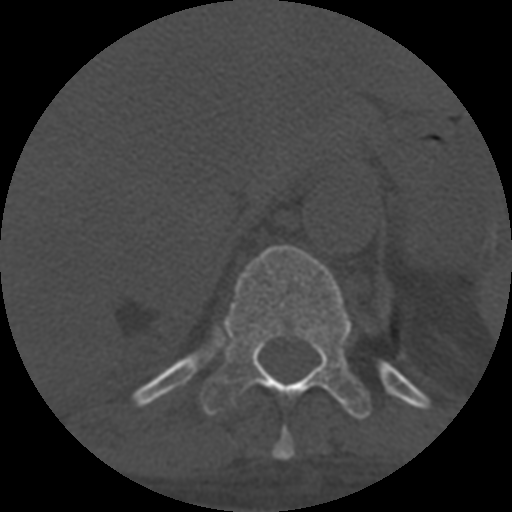
CT including the spine, one axial slice; slice 340 of 708 in the series (ordered by position); reconstruction kernel STANDARD; 120 kVp; one of 3 acquisitions stored at this slice position; bone window (W 1800 / L 400 HU); 512 × 512 image matrix. Patient age 55 years. Case-level facts recorded for this patient, not image findings: primary cancer: colon; vertebrae with lytic lesions (as recorded): T12, L1, L5.
Structures marked on this image (semi-automatic segmentation, software-assisted and operator-edited):
- T10 vertebra: bounding box (x1, y1, x2, y2) in pixels: (272, 427, 295, 460)
- T11 vertebra: (201, 245, 371, 420)